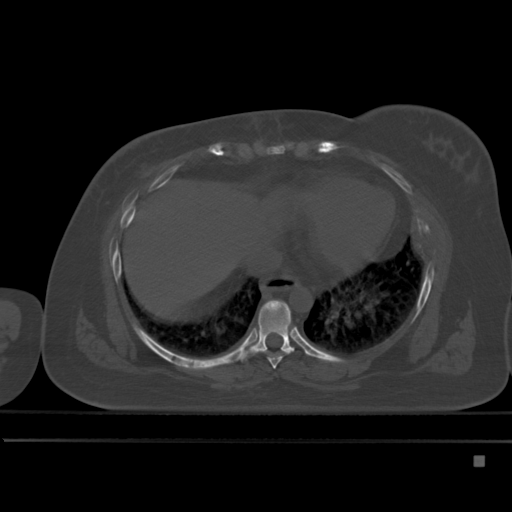
CT including the spine, one axial slice; slice 283 of 495 in the series (ordered by position); bone window (W 1800 / L 400 HU); 1.5 mm slice thickness; 512 × 512 image matrix, field of view 404 × 404 mm. Female patient, age 33 years. From the clinical record (not read from this slice): primary cancer: breast; vertebrae with lytic lesions (as recorded): T1.
Outlined on this slice (semi-automatic segmentation, software-assisted and operator-edited):
- T7 vertebra: box from (x=268, y=327) to (x=296, y=369) px
- T8 vertebra: (x=236, y=300)–(x=295, y=362)